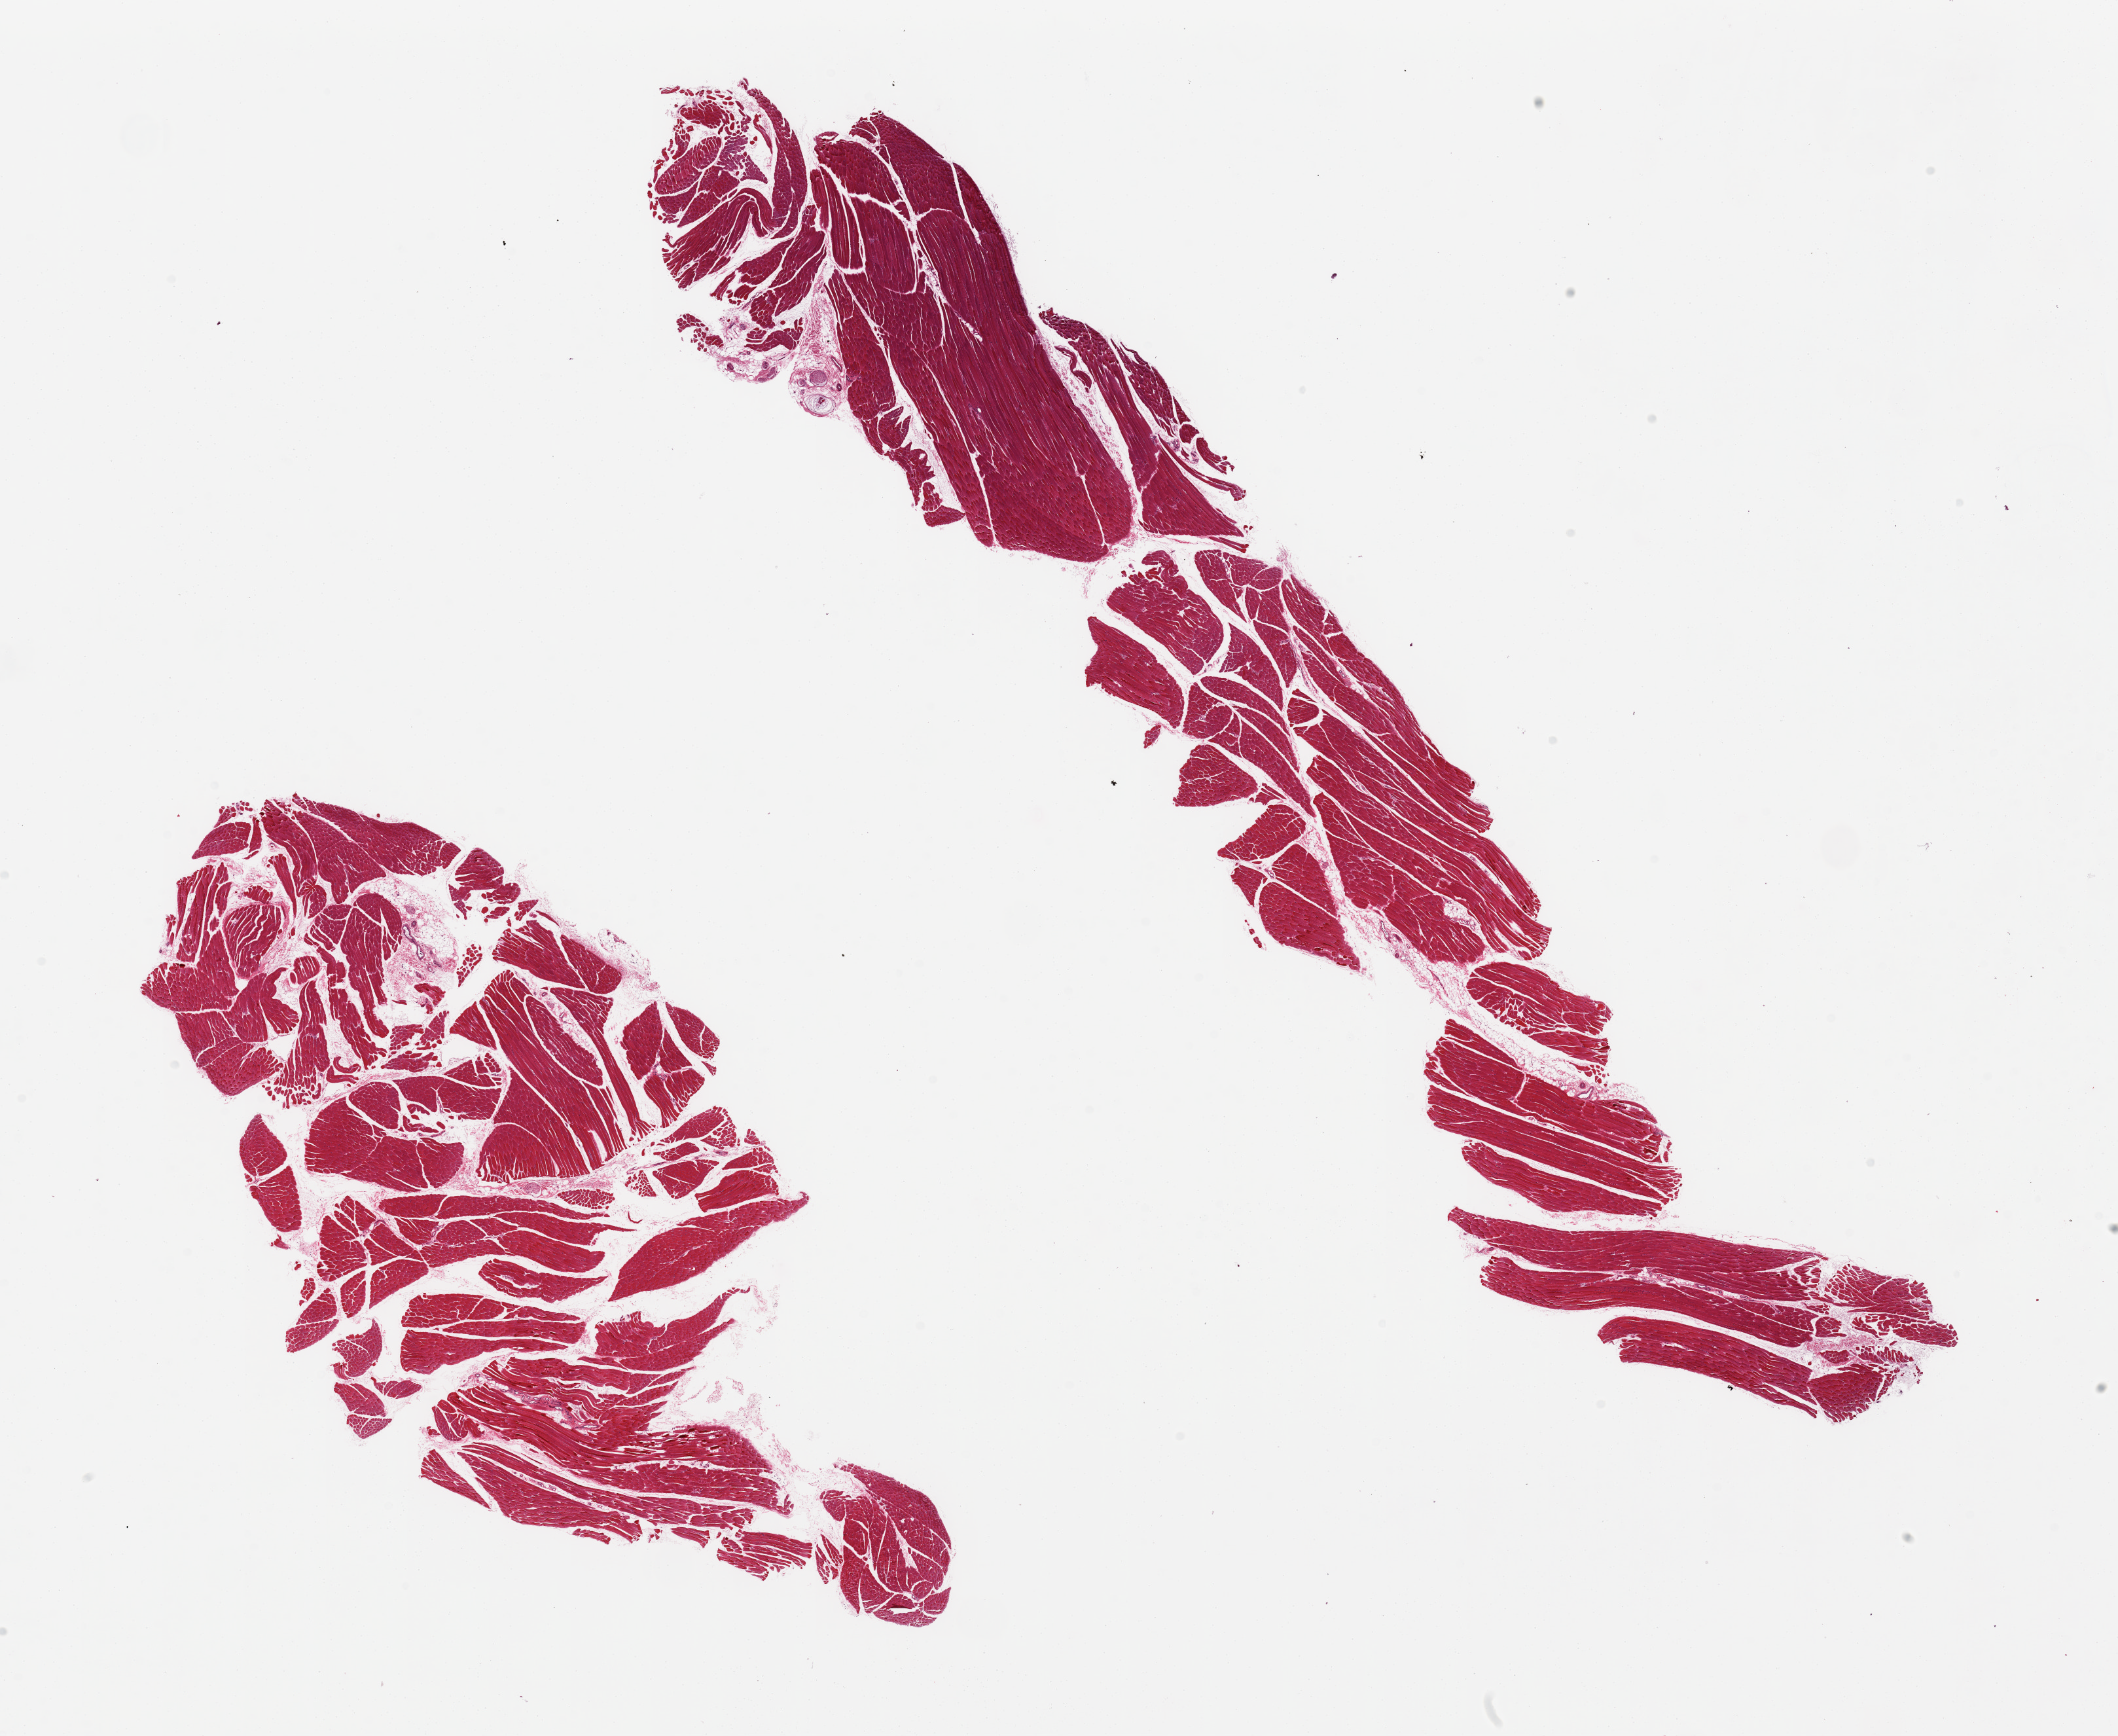
Whole-slide image, H&E stain, brightfield — whole scanned area (about 25.6 x 21.0 mm, slide scanned at 20x) shown as a low-resolution overview; PAXgene-fixed paraffin-embedded (PFPE) section; sampled site (target tissue): skeletal muscle; donor tissue sample. Female donor.
Reviewer comment on this tissue sample: 2 pieces, 5-10% internal adipose tissue and nerve.